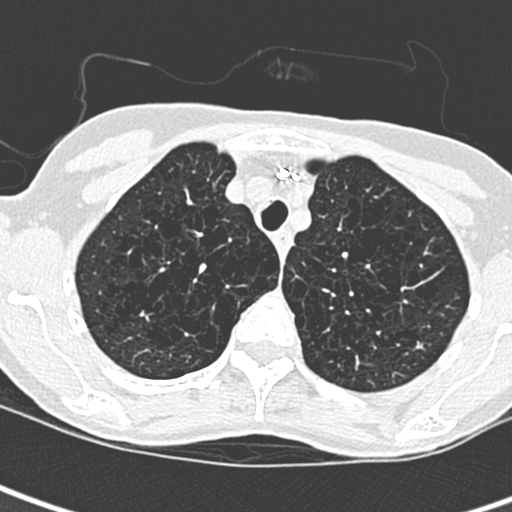
Low-dose screening chest CT, axial slice; baseline screening round; lung window (W 1500 / L -600 HU); 1.3 mm slice thickness; lung (sharp) reconstruction kernel (D); 120 kVp; slice 53 of 259 in the series. Female, age 71 years at enrolment. Current smoker at enrolment.
Lesion marked by an expert reader, bounding box [x1, y1, x2, y2] px = [398, 327, 436, 365]. Screening reader's record for this exam: no non-calcified nodule ≥4 mm recorded. Official screen result: negative screen, no significant abnormalities. Participant outcome: lung cancer diagnosed 975 days after this screen (after the third annual screen) — adenocarcinoma, NOS, left upper lobe, moderately differentiated (G2), stage IA (AJCC 6th edition), 12 mm at pathology.